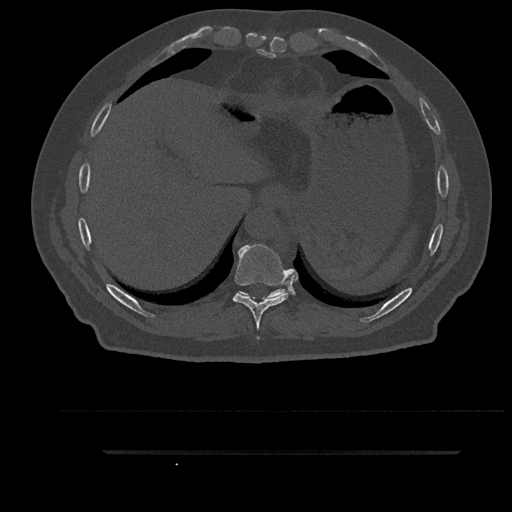
CT including the spine, one axial slice. Position 411 of 797 along the scan axis. Reconstruction kernel Br40s/3. Bone window (W 1800 / L 400 HU). 512 × 512 image matrix. Patient: male, 63 years. Case-level facts recorded for this patient, not image findings: primary cancer: renal.
Structures marked on this image (semi-automatically segmented with operator editing):
- T10 vertebra: bounding box (x1, y1, x2, y2) in pixels: (237, 289, 286, 298)
- T9 vertebra: (233, 244, 291, 339)